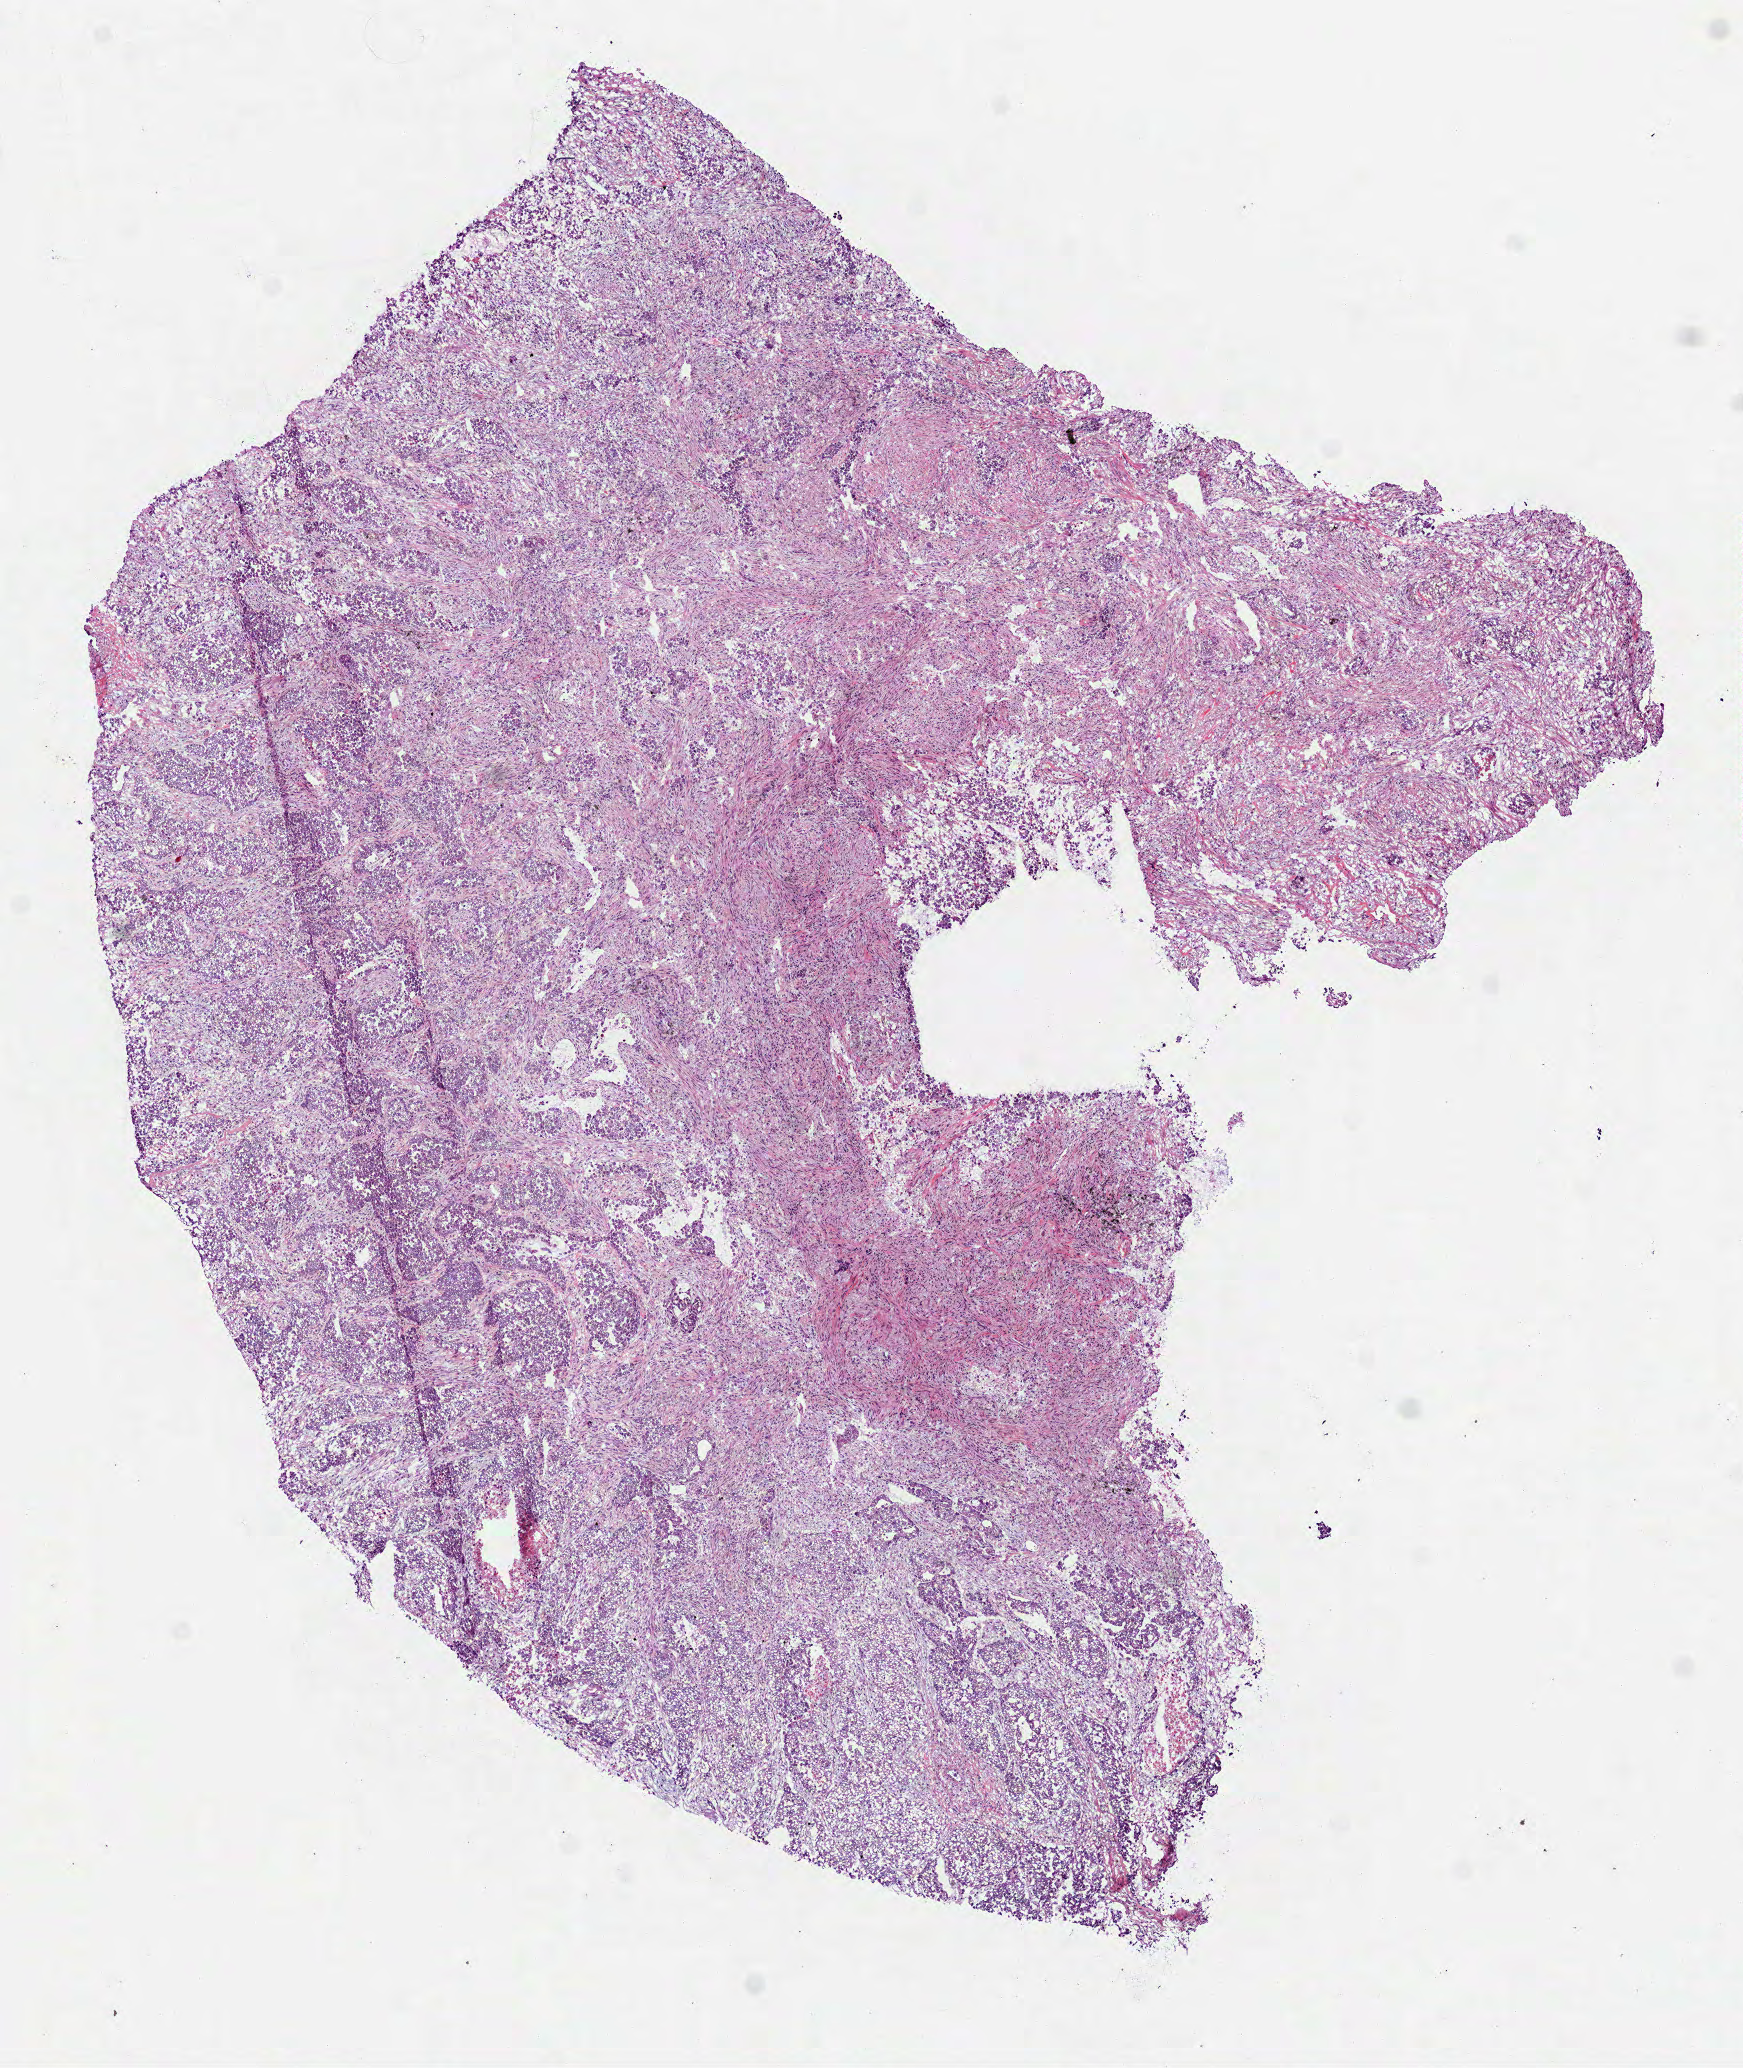
Whole-slide histology image, Hematoxylin and eosin (H&E) stained — a low-resolution overview of the entire scanned area, about 7.0 x 8.3 mm (acquisition: 40x scan). Frozen section from the bottom of the tissue portion. Lung, primary tumour sample. Patient: male, age at initial diagnosis 58 years. Pathologist review of this section (percent, as recorded): tumour cells 99%, tumour nuclei 70%.
Diagnosis: Adenocarcinoma, NOS (upper lobe, lung).